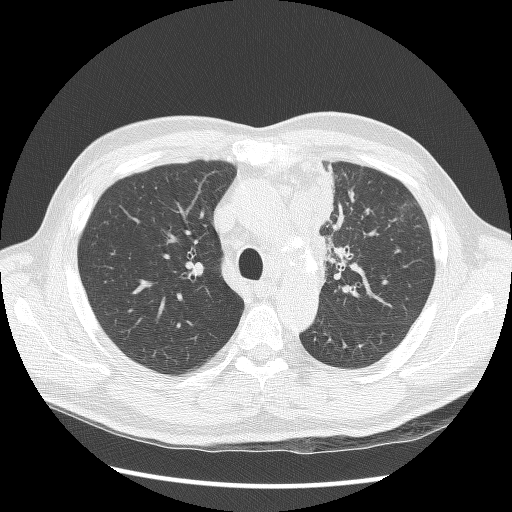
Low-dose screening chest CT, axial slice; second annual screen; lung window (W 1500 / L -600 HU); 2.5 mm slice thickness; lung (sharp) reconstruction kernel (BONE); slice 38 of 136 in the series. Male, age 64 years at enrolment. Former smoker at enrolment.
Expert-annotated lung lesion, bounding box <297,170,368,291> (left, top, right, bottom; pixels). Screening reader's record for this exam: no non-calcified nodule ≥4 mm recorded. Official screen result: positive, other. Lung cancer was diagnosed 24 days after this screen: small cell carcinoma, NOS, left upper lobe, stage IV (AJCC 6th edition), 100 mm at pathology.